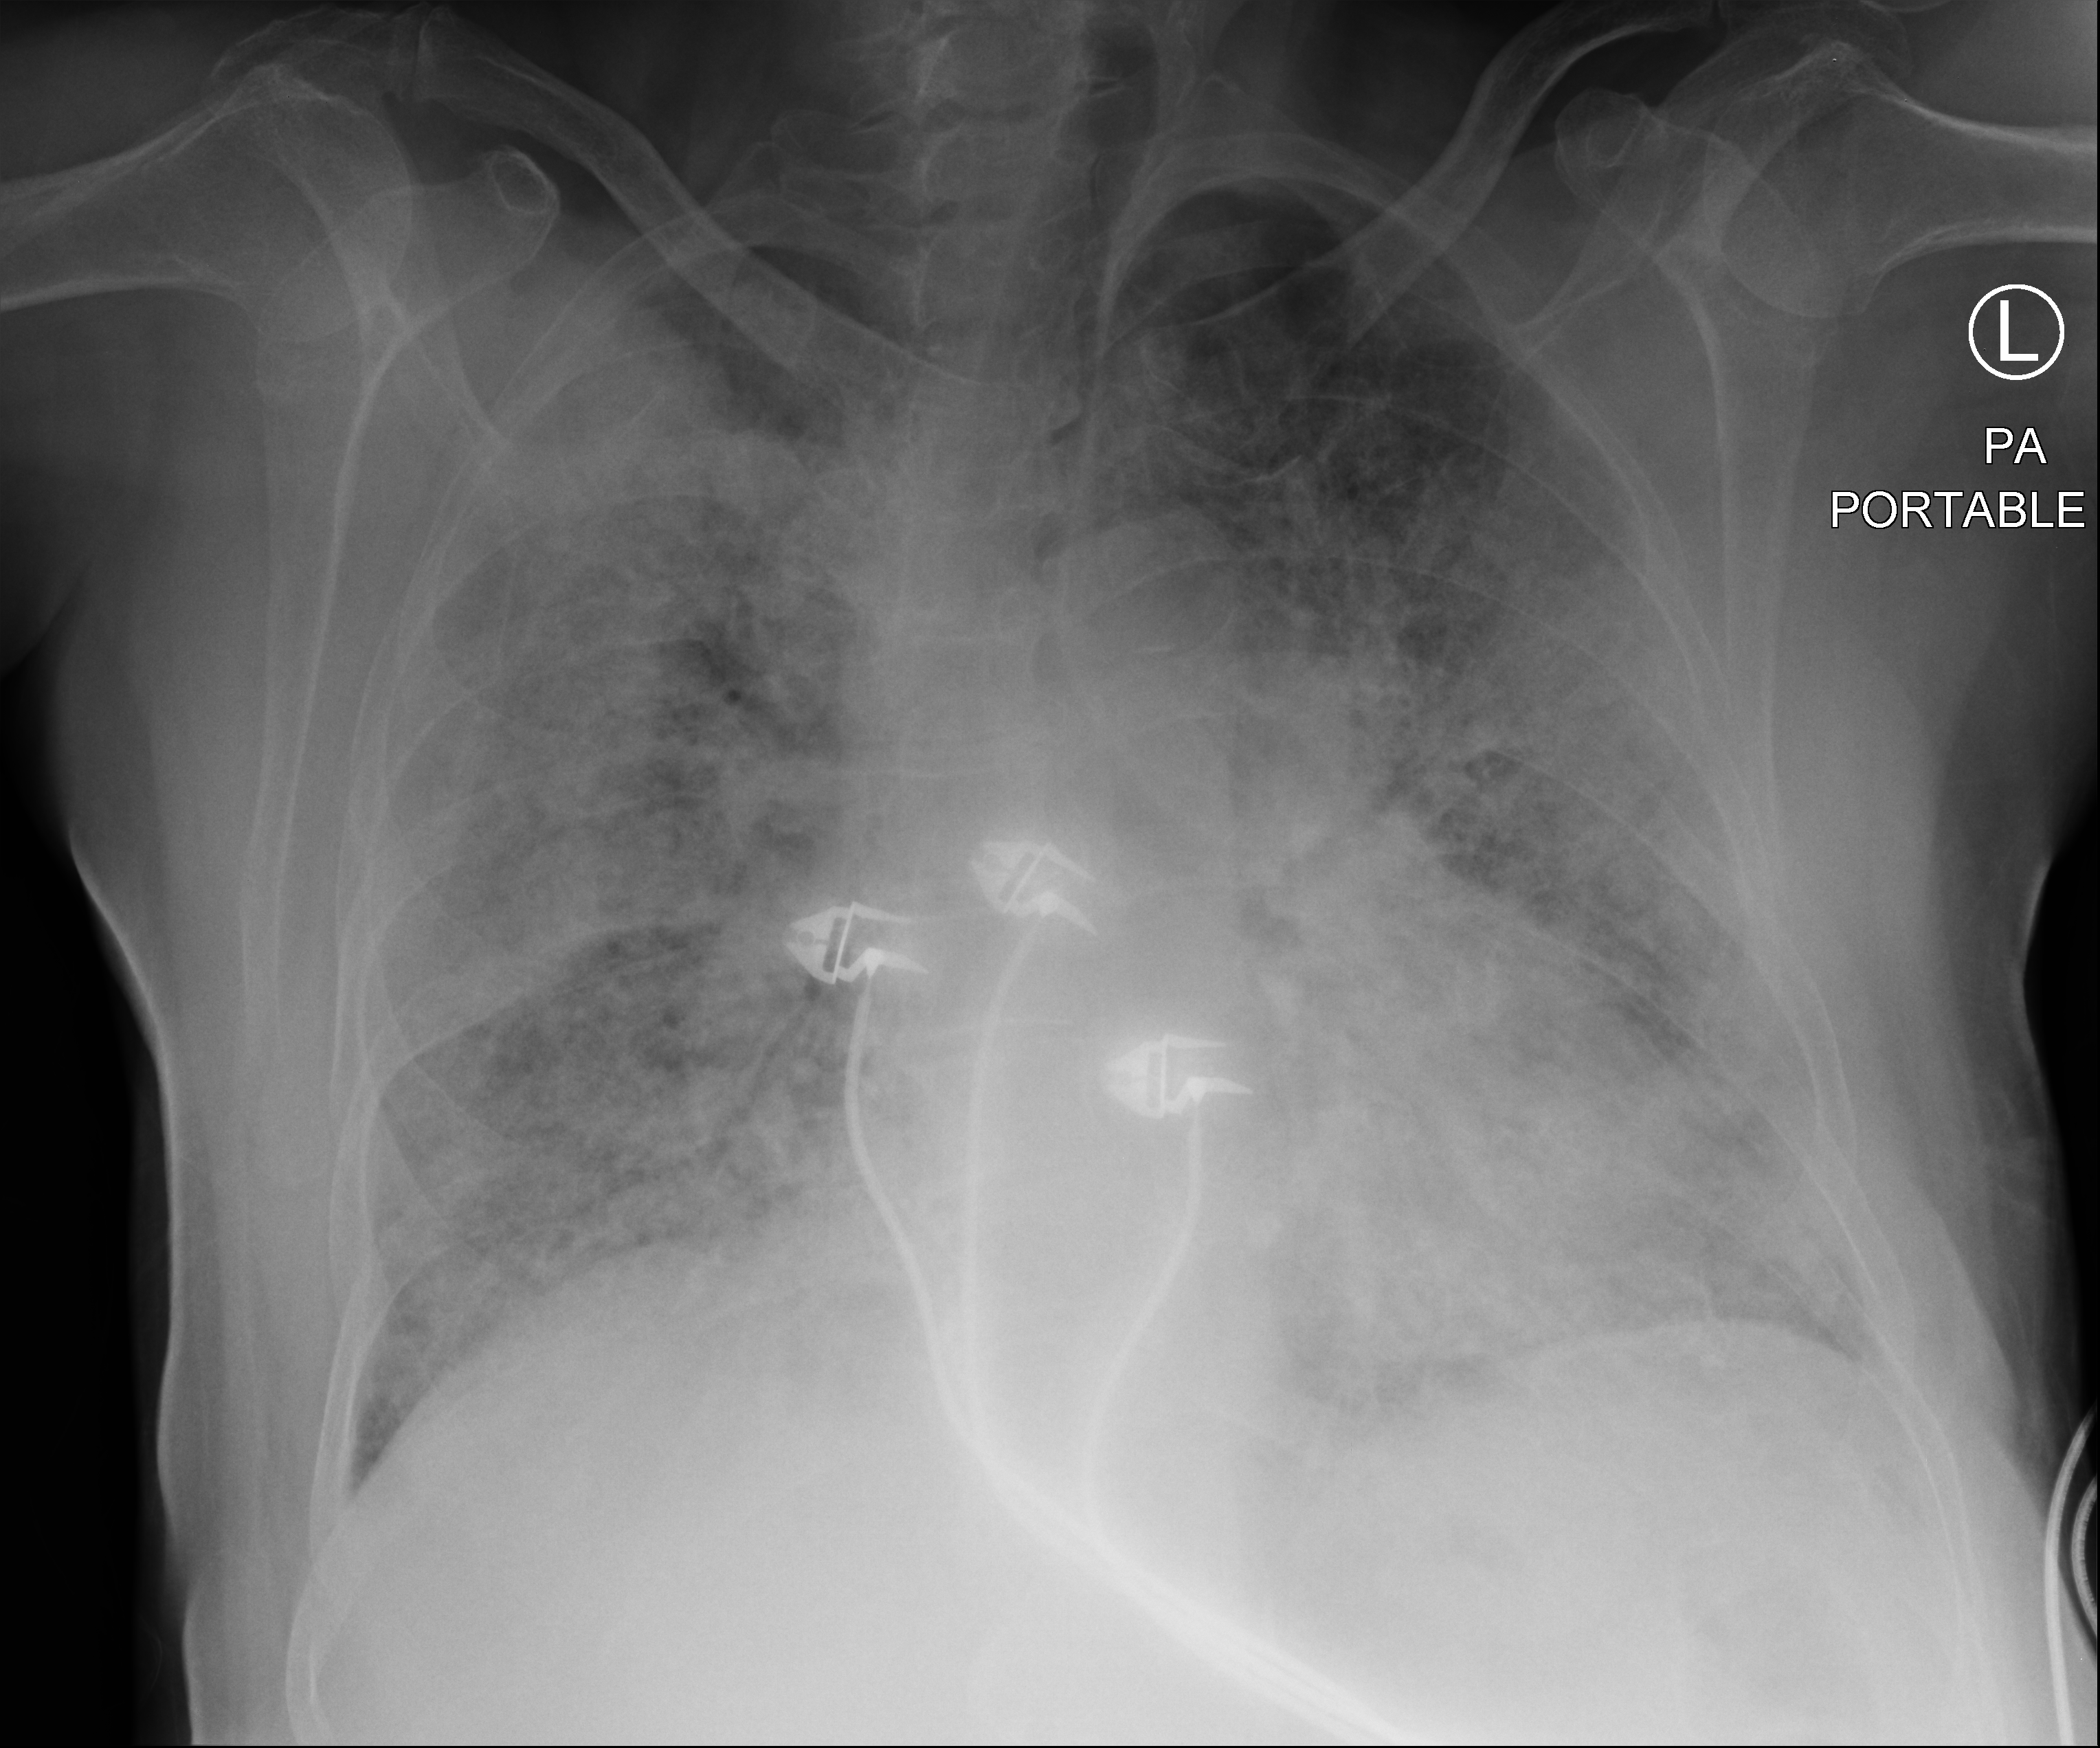
Chest X-ray (portable); posteroanterior (PA) projection. Male patient hospitalised with COVID-19, age 75–90 years.
Hospital-stay facts (about this admission, not read from this image; timing relative to this image not recorded): admitted to intensive care during this hospital stay: yes.